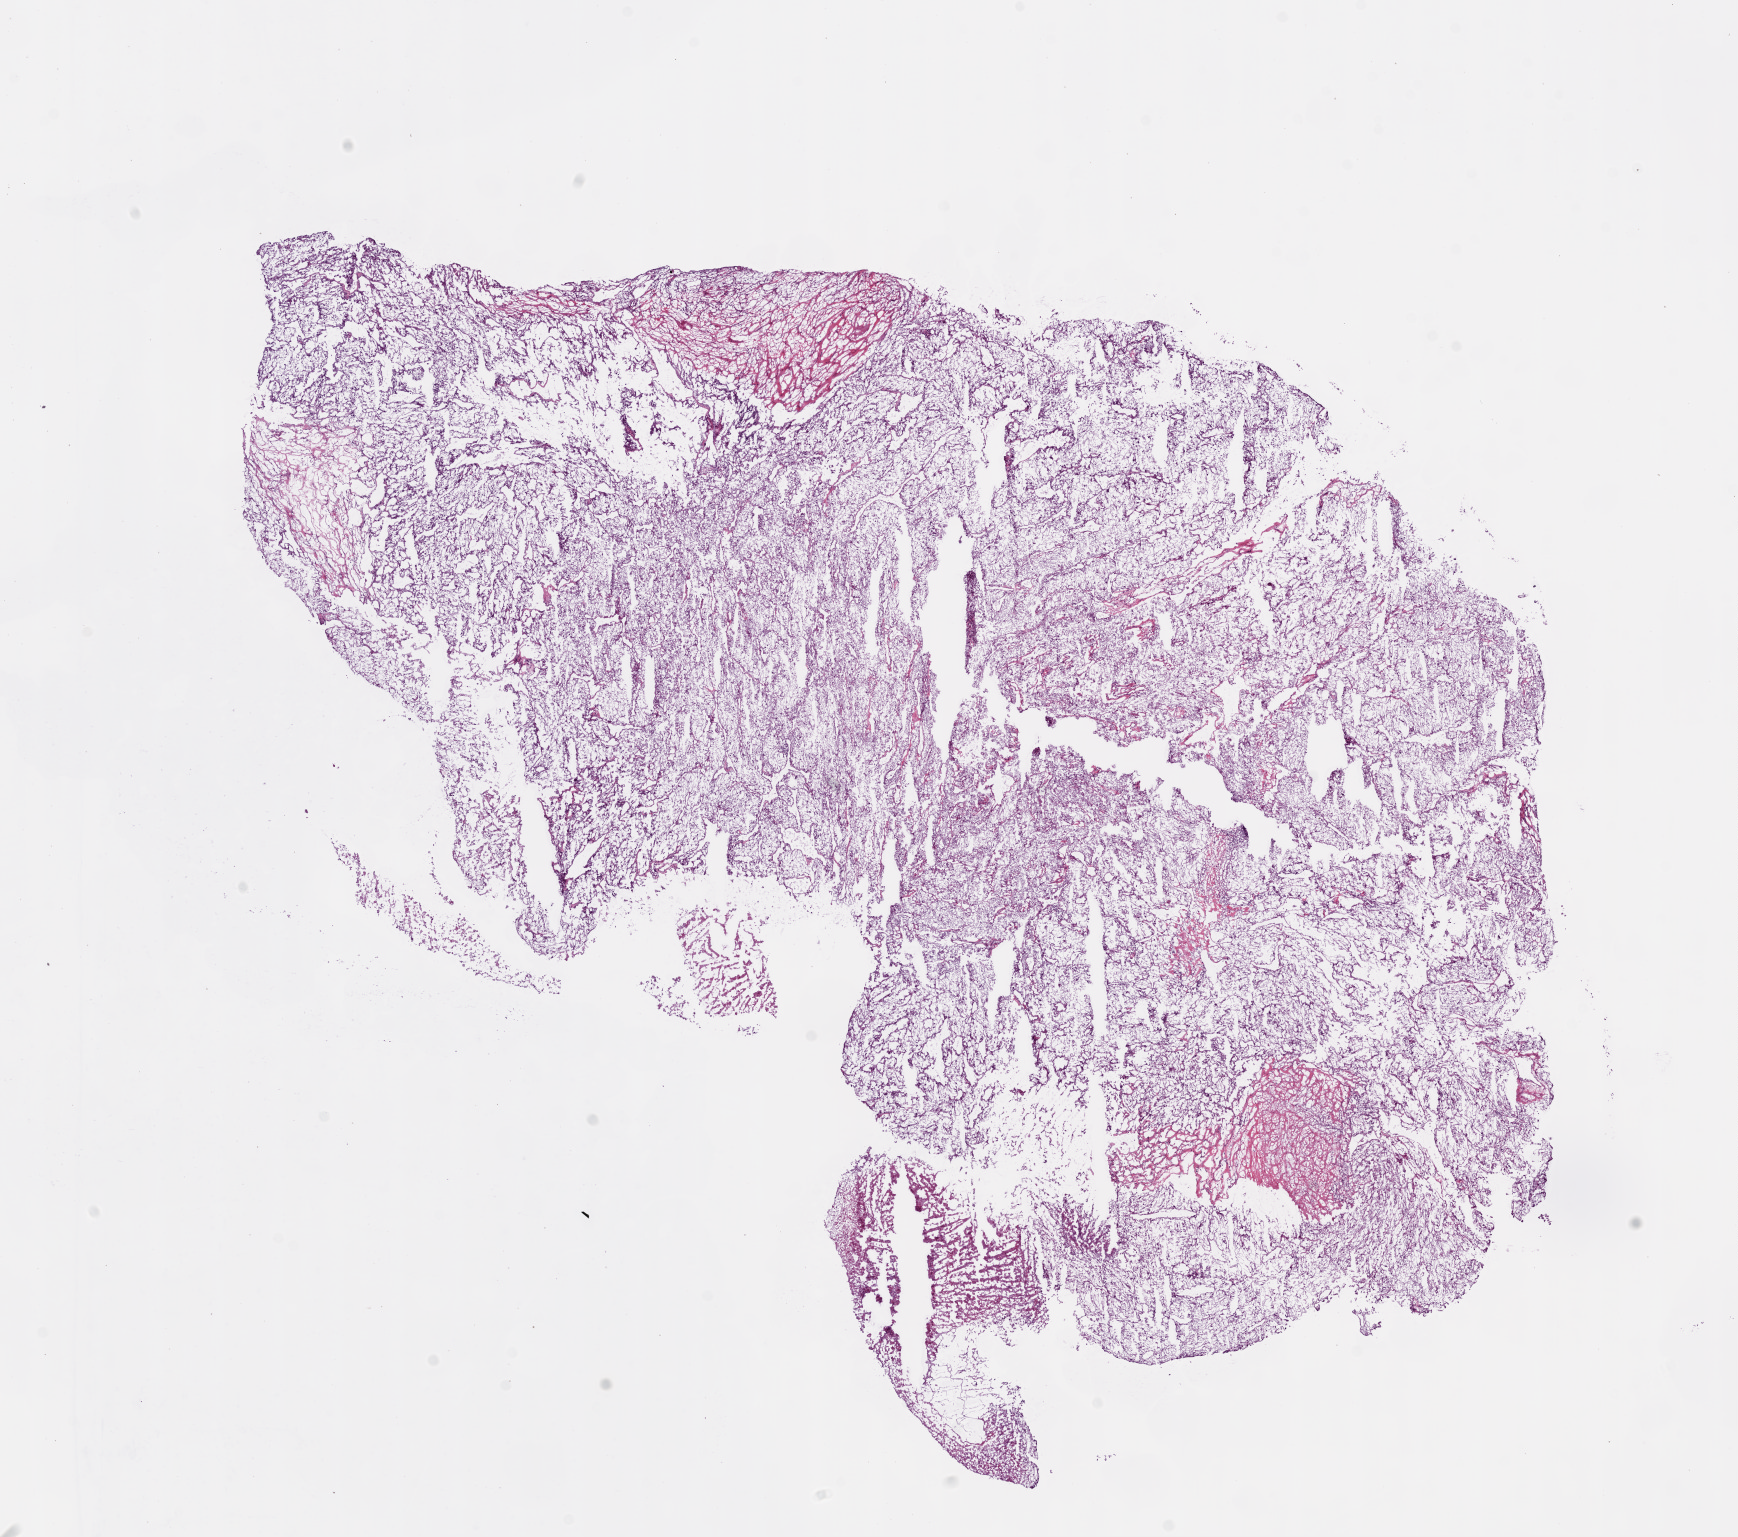
H&E-stained whole-slide image, low-resolution overview of the scanned area, about 14.0 x 12.4 mm. Frozen section. Primary tumour sample from the kidney. Male, age 65 years at initial diagnosis. Histologic grade: G2 (moderately differentiated). Pathologist review of this section (percent, as recorded): tumour cells 90%, tumour nuclei 90%, normal cells 0%, stromal cells 10%, necrosis 0%. Inflammatory infiltration, as recorded: lymphocyte infiltration 1%, monocyte infiltration 0%, neutrophil infiltration 0%.
AJCC pathologic stage: III (7th edition). Pathologic diagnosis: Clear cell adenocarcinoma, NOS.